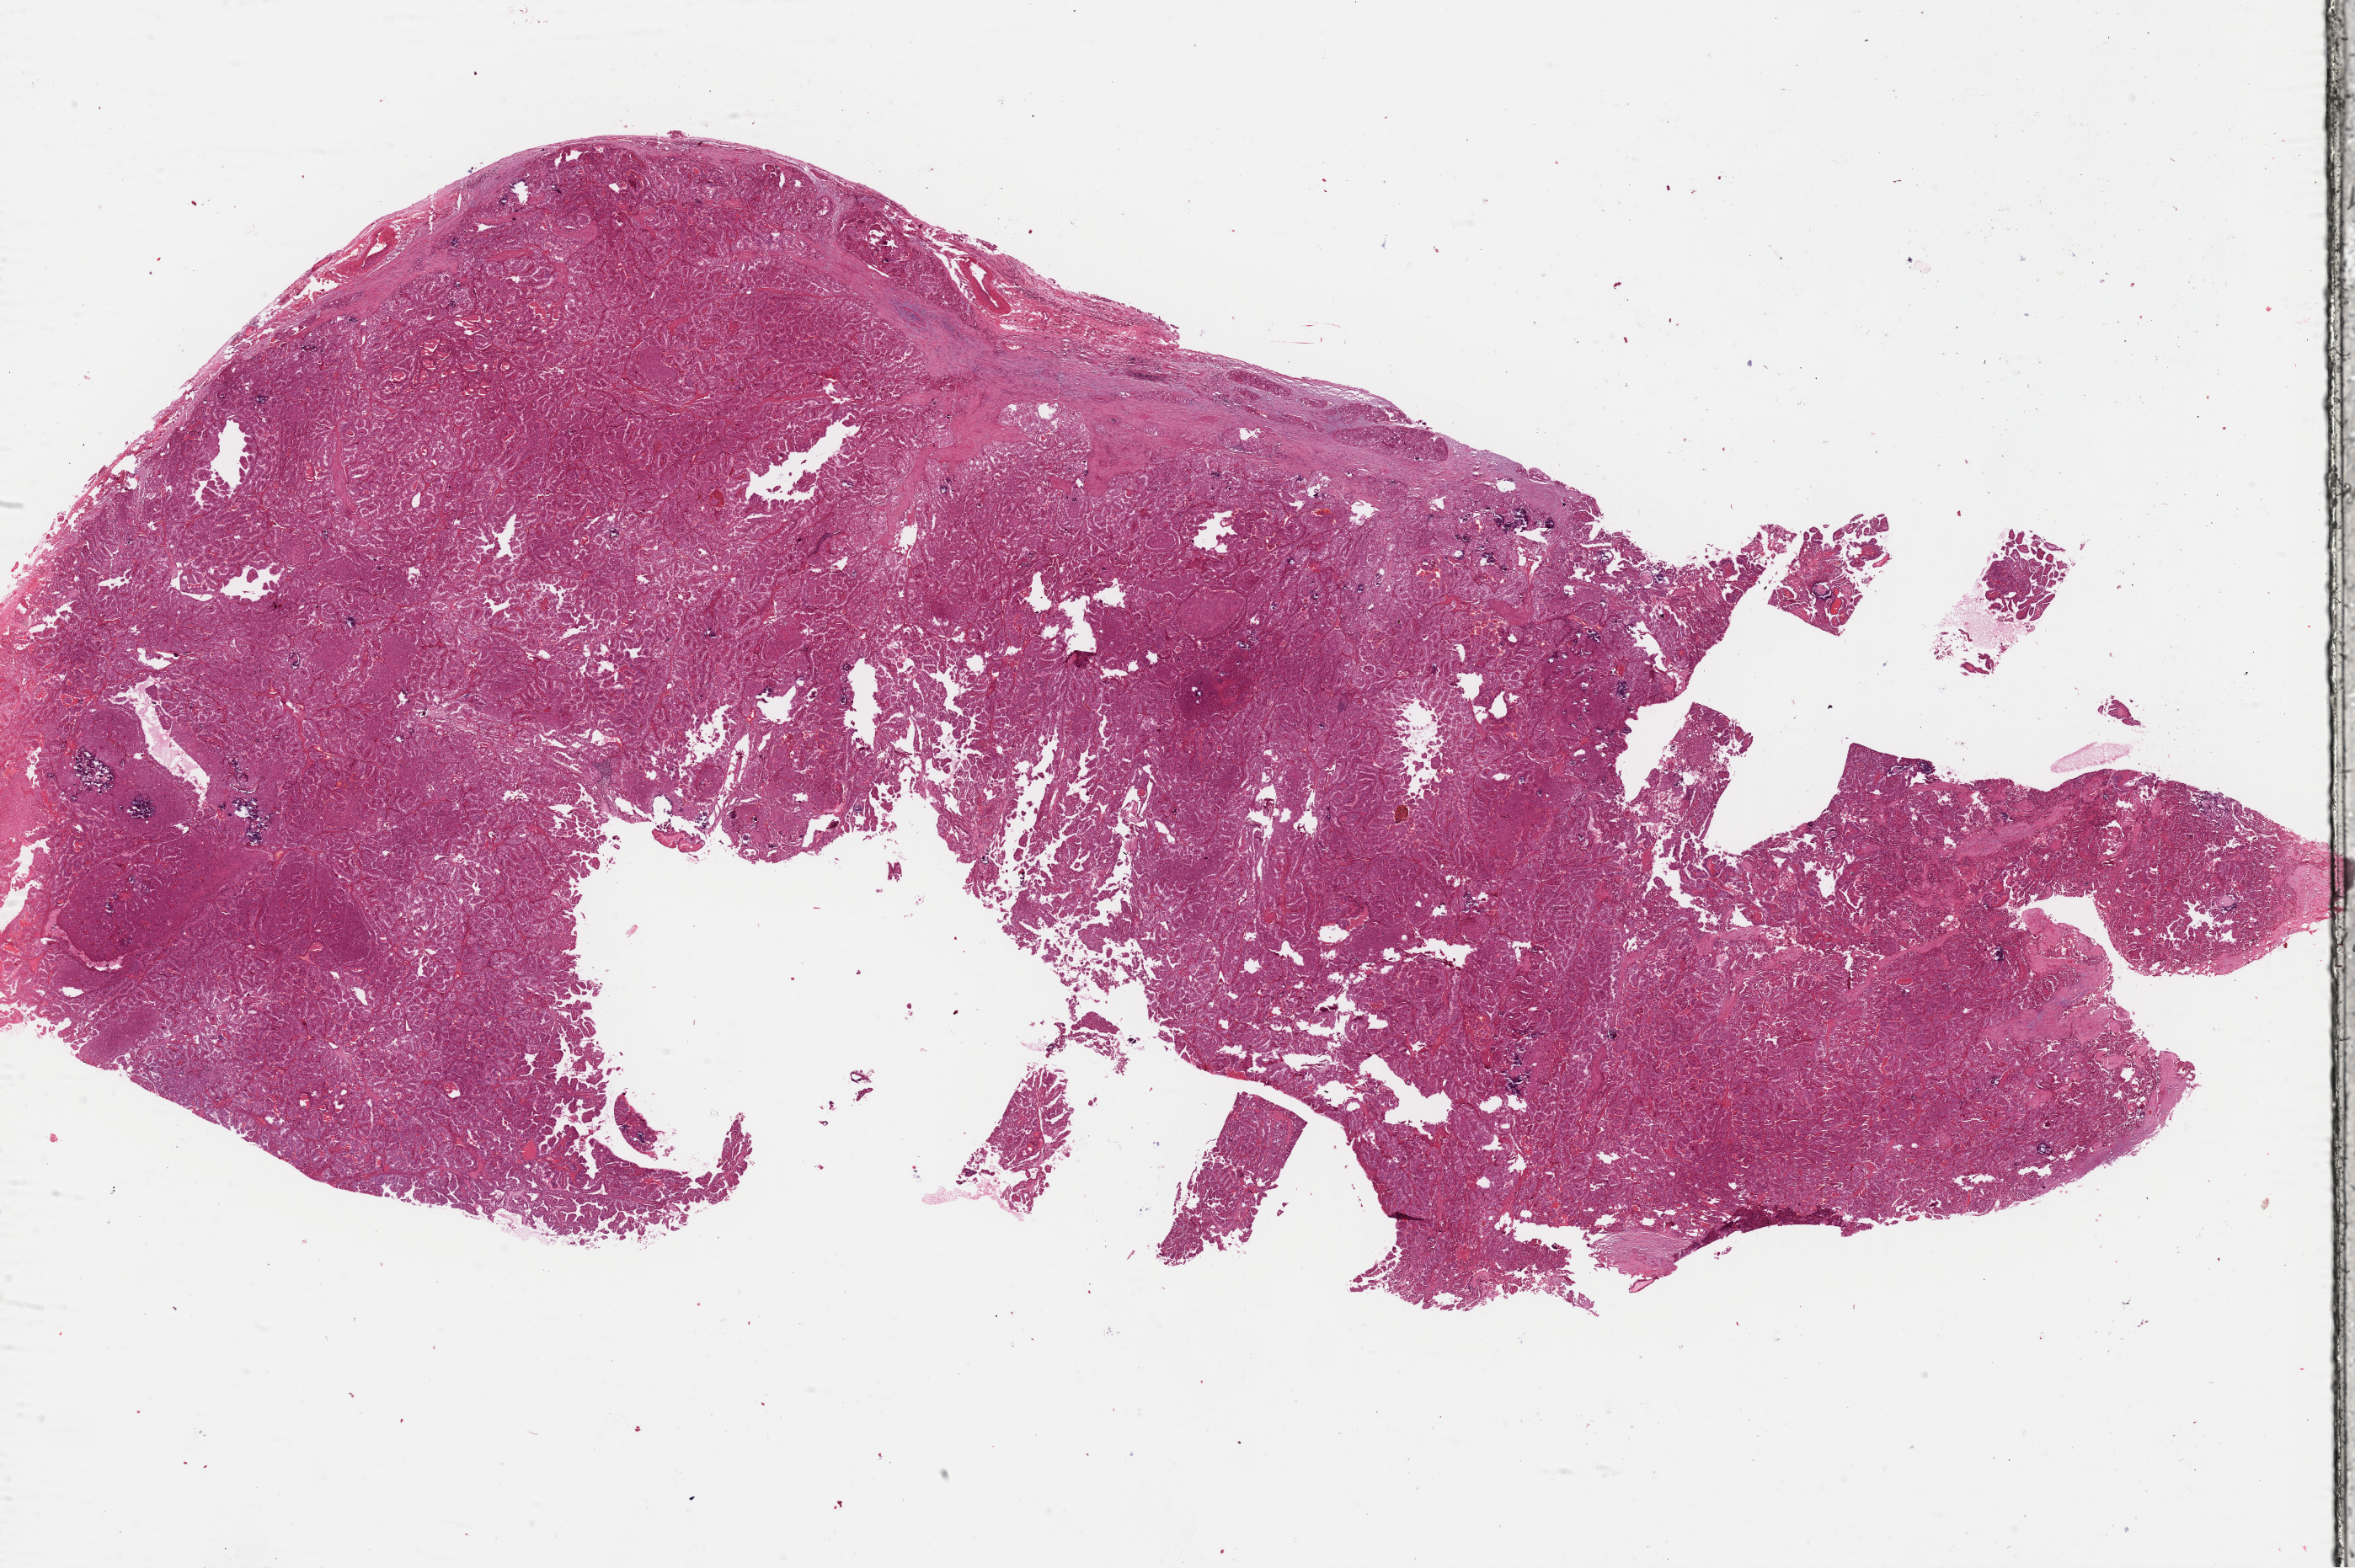
H&E whole-slide image, a low-resolution overview of the entire scanned area, about 22.1 x 14.7 mm (slide scanned at 40x), formalin-fixed paraffin-embedded (FFPE) diagnostic section, sample: primary tumour, thyroid. Patient: female, age at initial diagnosis 27 years.
AJCC pathologic stage: I (7th edition). Laterality: right. Histologic diagnosis: Papillary adenocarcinoma, NOS (thyroid gland).